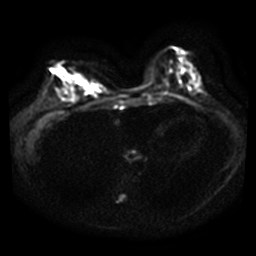
Breast MRI, one axial slice; position 12 of 40 along the scan axis; diffusion-weighted series; image 2 of 4 stored at this slice position (different b-values; order by instance number); 3 T; 5 mm slice thickness; 256 × 256 image matrix, field of view 340 × 340 mm. Female patient.
Outlined on this slice (expert manual segmentation):
- tumour on diffusion-weighted imaging: bounding box [x1, y1, x2, y2] px = [56, 65, 100, 95]